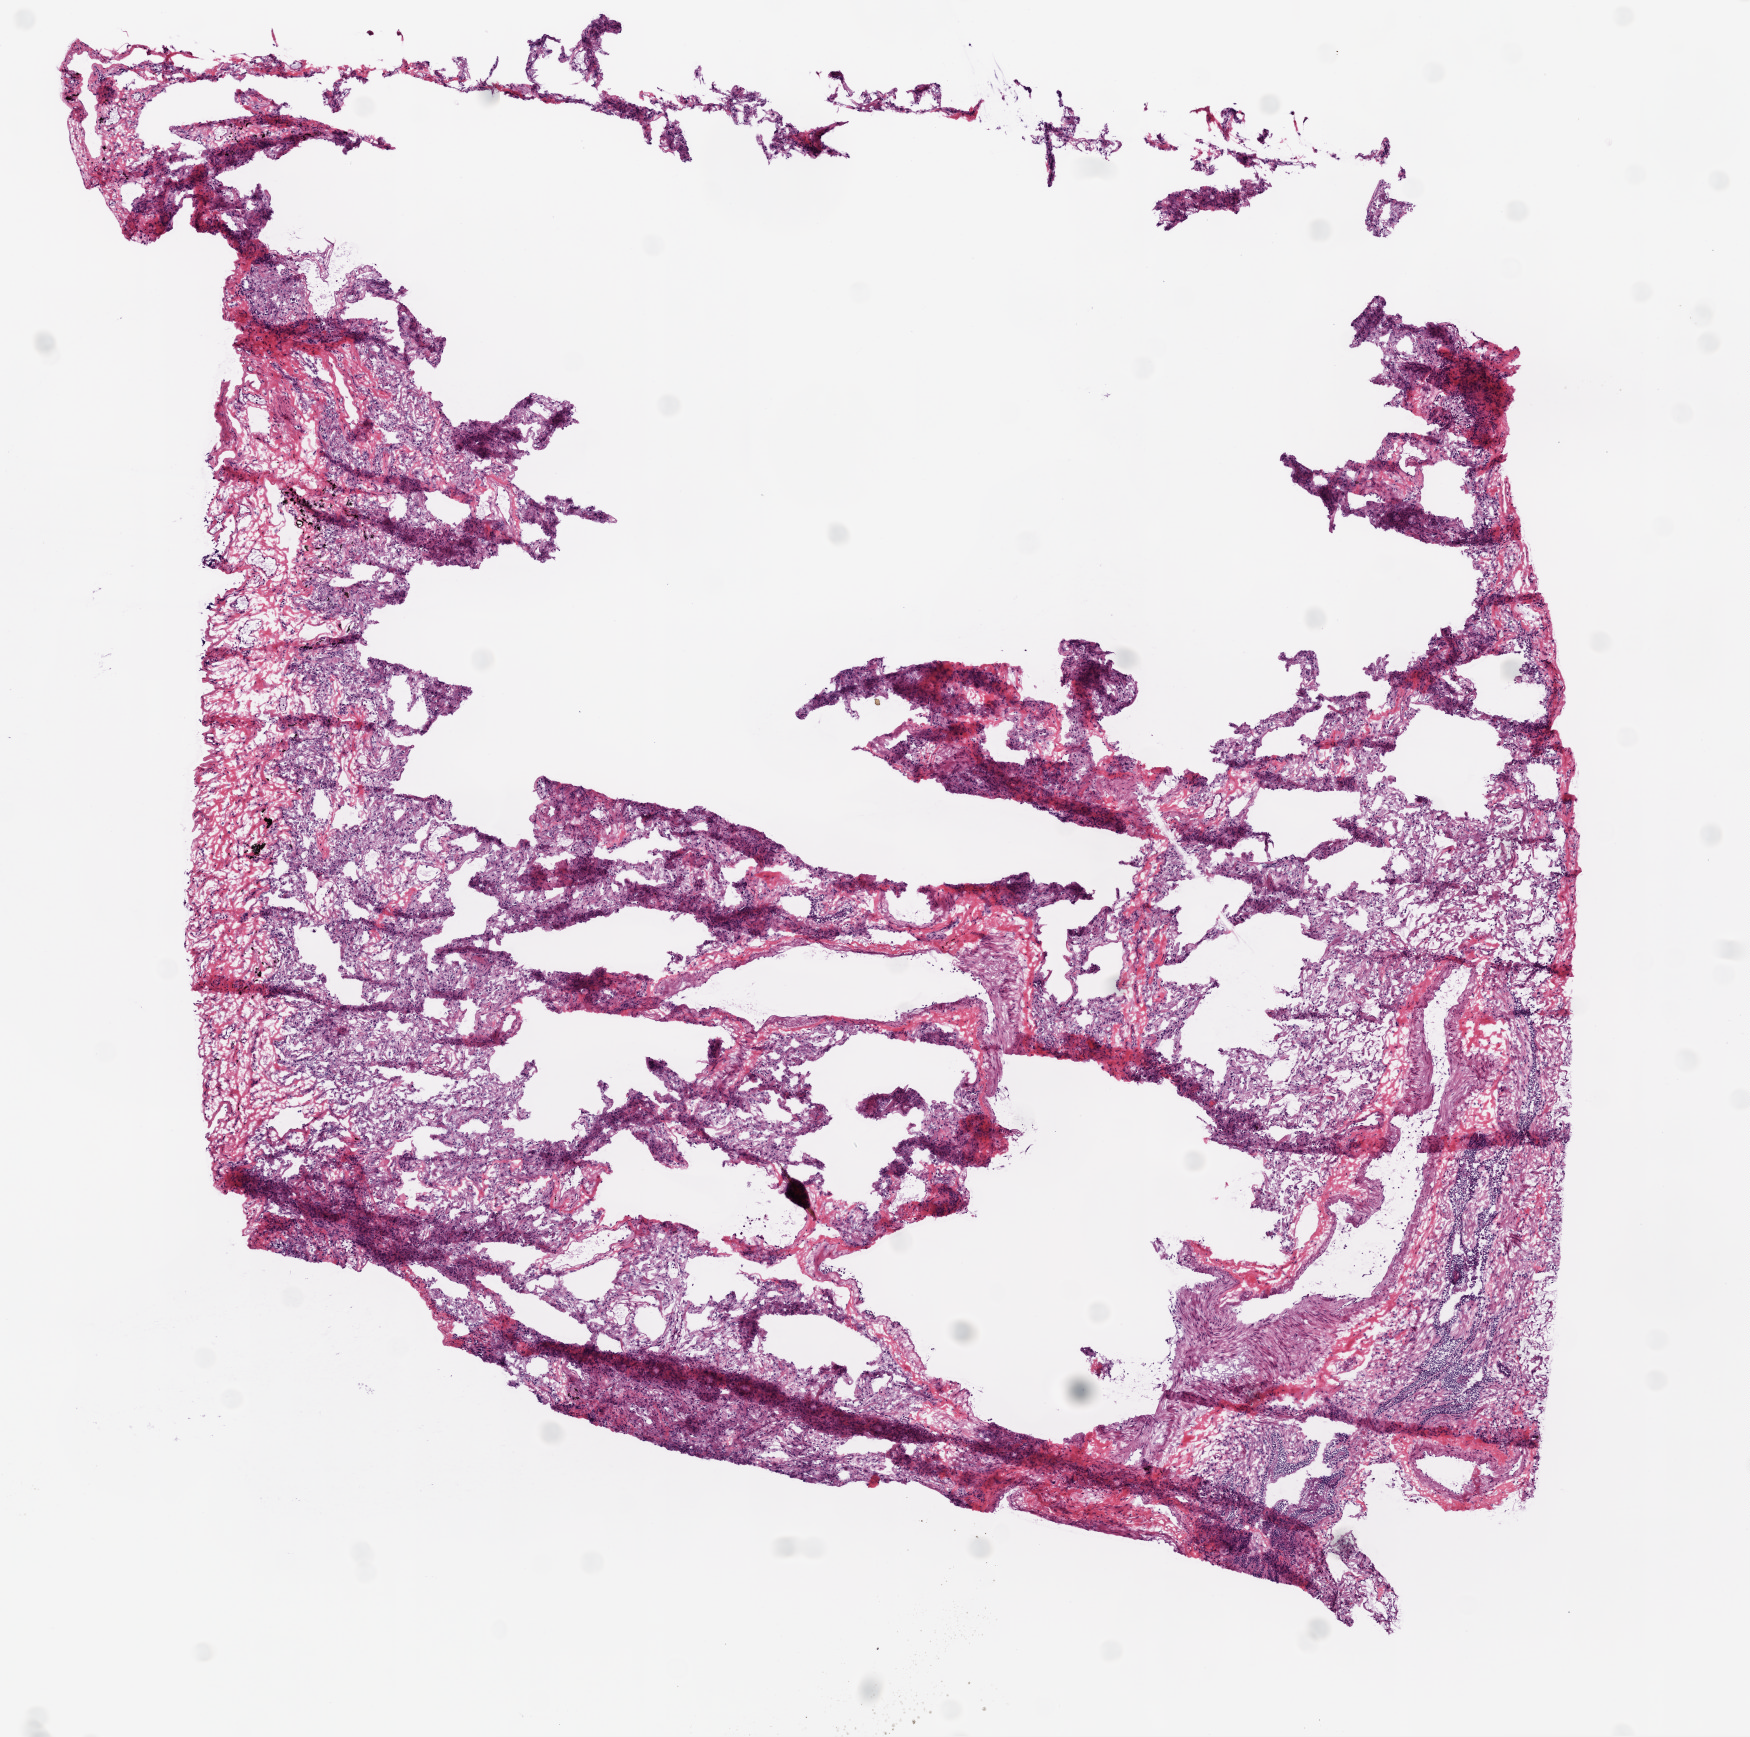
Whole-slide histology image, H&E-stained — shown as a low-resolution overview of the whole scanned area (about 7.0 x 7.0 mm); frozen section from the top of the tissue portion; sample: solid tissue normal (non-tumour tissue), lung. Patient: male, age at initial diagnosis 66 years.
This section: solid tissue normal (non-tumour) sample from the same patient. Patient diagnosis: Squamous cell carcinoma, NOS (upper lobe, lung).